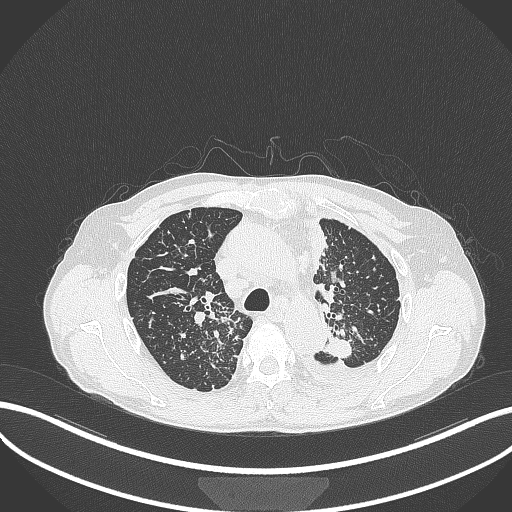
Chest CT, one axial slice. Position 255 of 325 along the scan axis. 120 kVp. Lung window (W 1500 / L -600 HU). 1 mm slice thickness. 512 × 512 image matrix, field of view 400 × 400 mm. Male patient, age 58 years. Case-level facts recorded for this patient, not image findings: clinical TNM (as recorded): T1c N3 M1.
Structures marked on this image (rectangle marked by the reading radiologist):
- lung tumour (recorded histology: adenocarcinoma): bounding box [x1, y1, x2, y2] px = [320, 328, 355, 359]